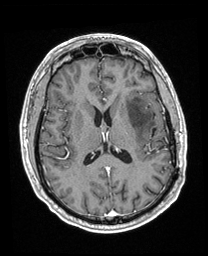
Brain MRI from a brain-tumour surgery series, one axial slice; slice 99 of 208 in the series (ordered by position); T1-weighted post-contrast; 1 mm slice thickness; 208 × 256 image matrix, field of view 211 × 260 mm. From the clinical record (not read from this slice): histopathology: Astrocytoma; WHO grade: 3; IDH mutation: yes.
Outlined on this slice (outlined manually by an expert reader):
- previous resection cavity: bounding box (x1, y1, x2, y2) in pixels: (151, 128, 156, 138)